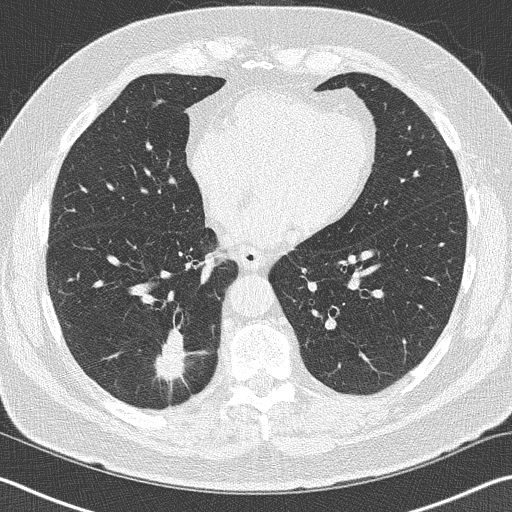
Chest CT (low-dose screening protocol), one axial image; first (baseline) screen; lung window (W 1500 / L -600 HU); lung (sharp) reconstruction kernel (B50f); slice 100 of 141 in the series; 512 × 512 image matrix, field of view 344 × 344 mm. Male participant, aged 70 years at enrolment. Current smoker at enrolment.
Expert-annotated lung lesion, bounding box (x1, y1, x2, y2) in pixels: (140, 326, 212, 399). The exam's reader record, not a measurement of the box and not confirmed to be the same lesion: non-calcified nodule or mass ≥4 mm, right lower lobe, 28 × 23 mm, spiculated (stellate) margins, soft tissue attenuation. Official screen result: positive, change unspecified: nodule(s) >= 4 mm or enlarging nodule(s), mass(es), or other non-specific abnormalities suspicious for lung cancer. Later outcome: lung cancer diagnosed 62 days after this screen — squamous cell carcinoma, NOS, right lower lobe, poorly differentiated (G3), stage IB (AJCC 6th edition), 24 mm at pathology.